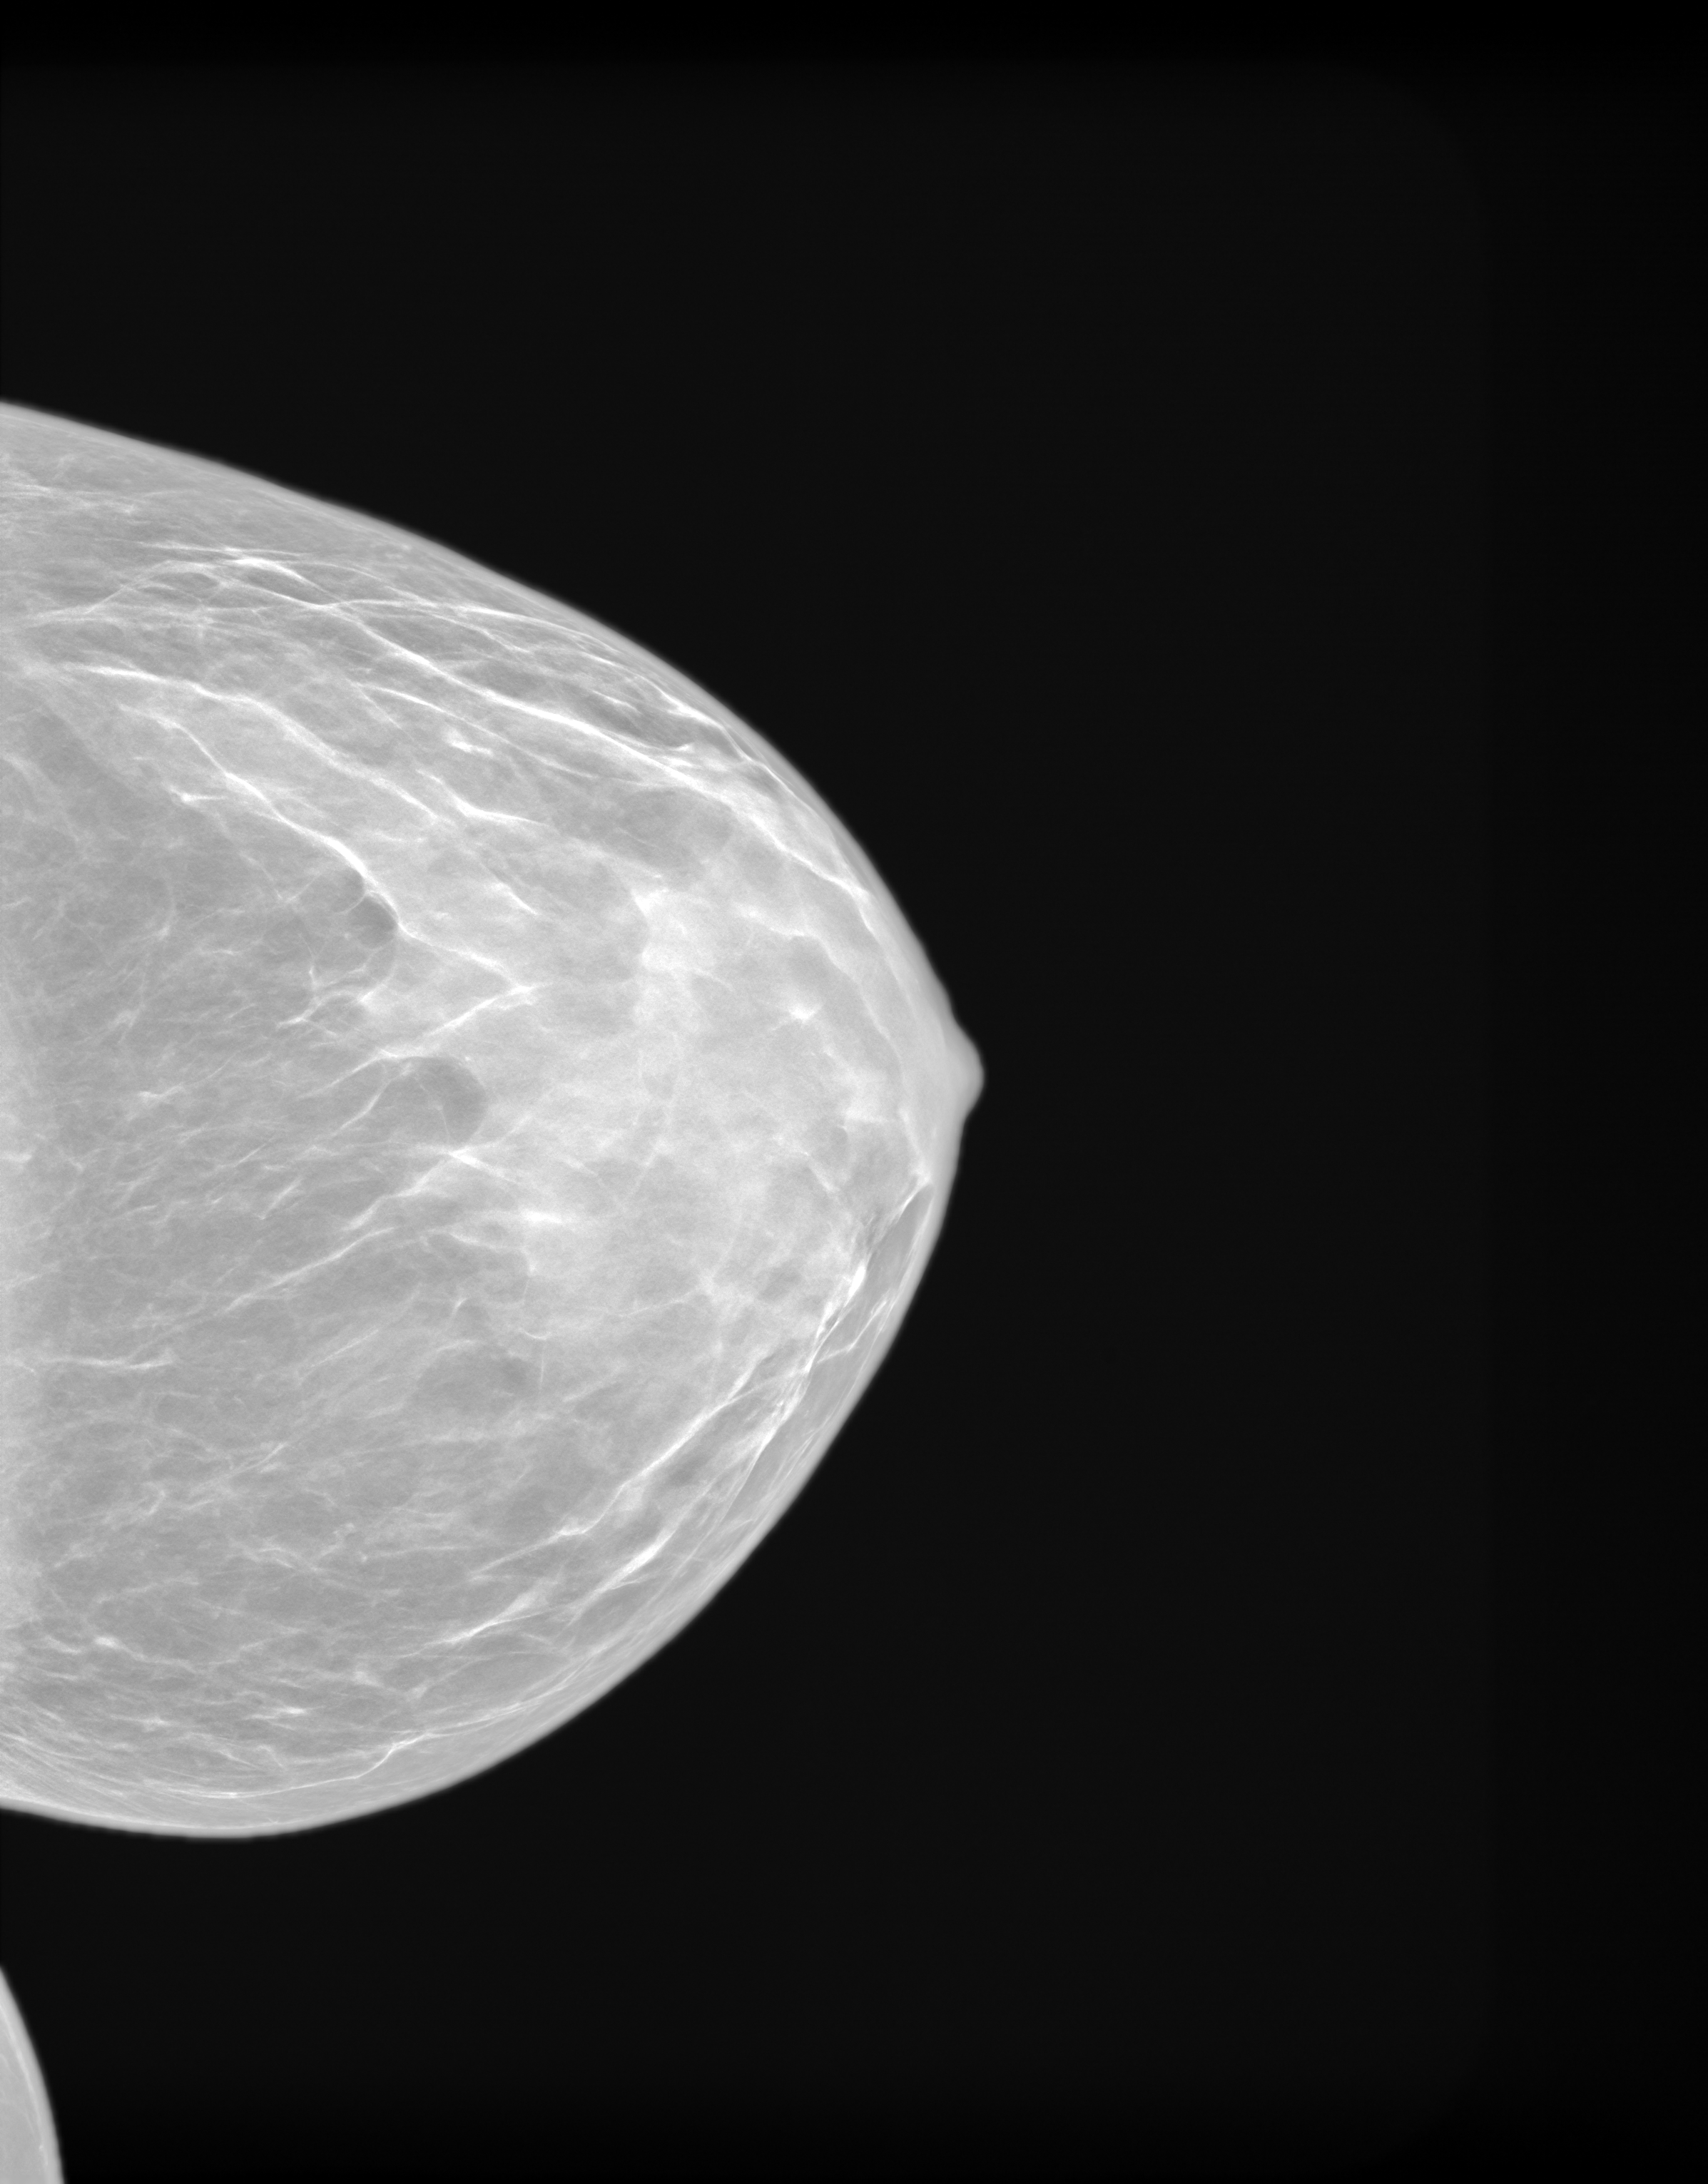
Annual screening mammography examination. Patient: female, 49 years.
Image type: synthesized 2-D view from tomosynthesis. Breast: left. Projection: cranio-caudal projection.